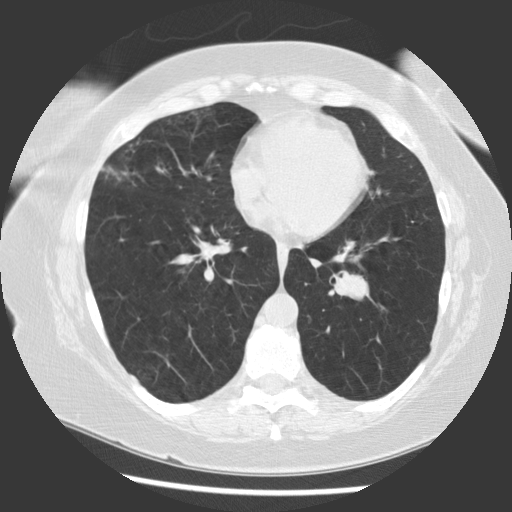
Low-dose screening chest CT, axial slice; baseline screening round; lung window (W 1500 / L -600 HU); 2.5 mm slice thickness; slice 57 of 130 in the series; 512 × 512 image matrix, field of view 340 × 340 mm. Female participant, aged 58 years at enrolment.
Expert reader's lesion annotation, bounding box (x1, y1, x2, y2) in pixels: (326, 258, 393, 321). Screening reader's record for this exam (one nodule recorded; not confirmed to be the boxed lesion): non-calcified nodule or mass ≥4 mm, left lower lobe, 22 × 15 mm, smooth margins, soft tissue attenuation.